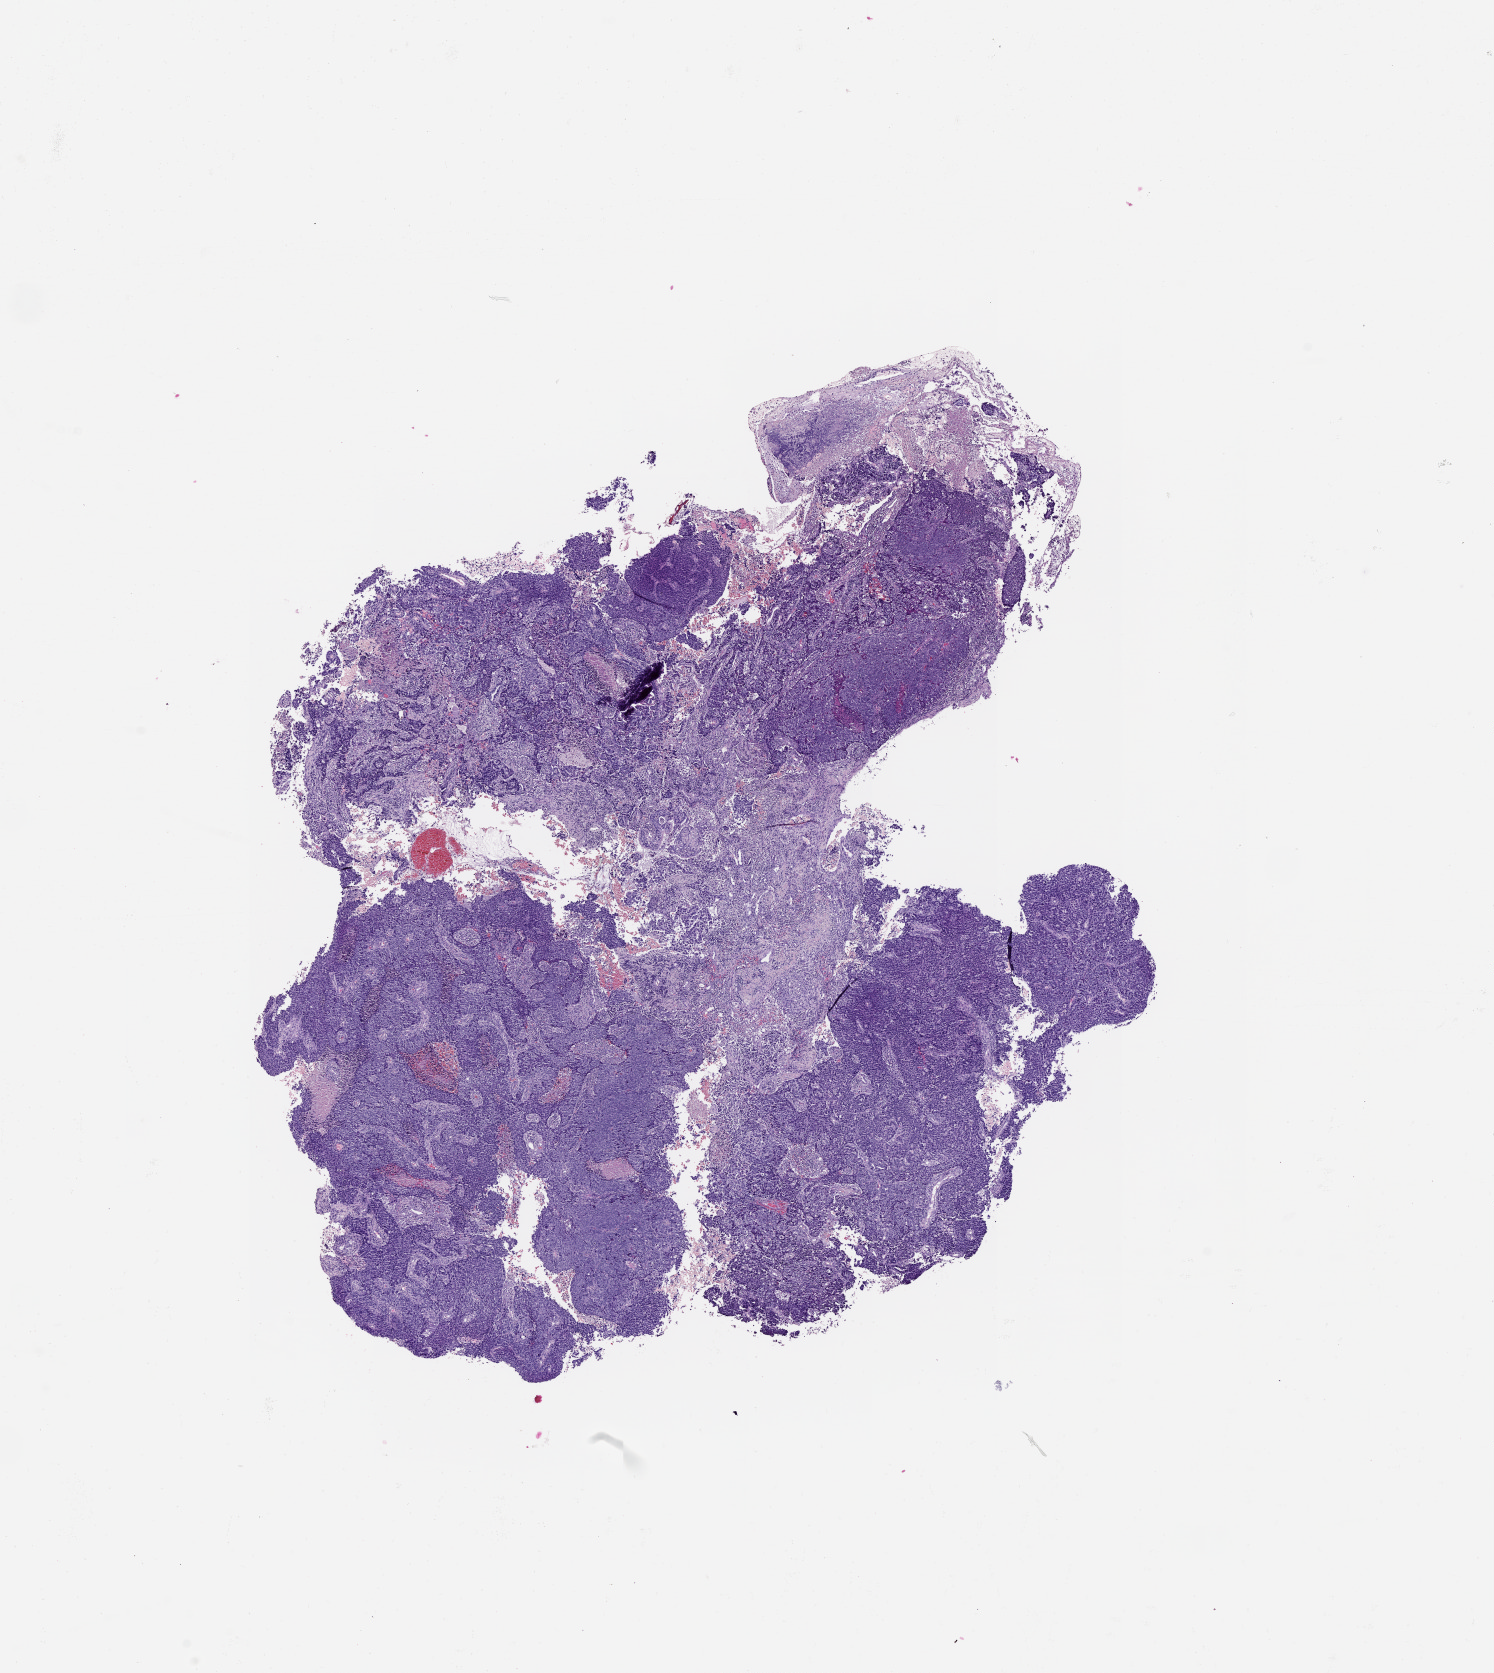
H&E-stained whole-slide image, low-resolution overview of the scanned area, about 12.0 x 13.5 mm (acquisition: 20x scan), tumour tissue sample, lung. Male, 60 y/o.
Patient diagnosis (cohort enrolment): squamous cell carcinoma (lung).